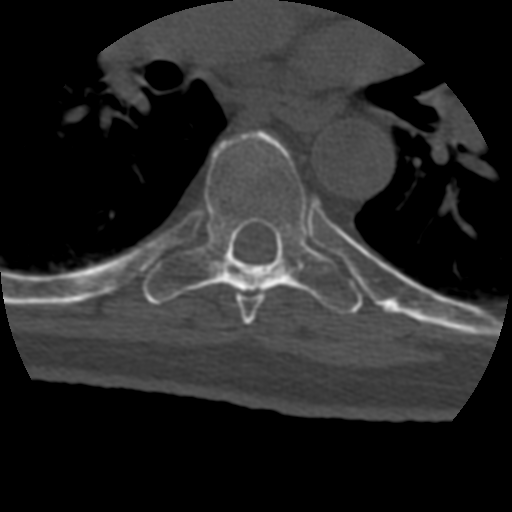
CT including the spine, one axial slice. Slice 287 of 399 in the series (ordered by position). Bone window (W 1800 / L 400 HU). 1.25 mm slice thickness. 512 × 512 image matrix. Patient age 69 years. Case-level facts recorded for this patient, not image findings: primary cancer: prostate.
Structures marked on this image (semi-automatic segmentation, software-assisted and operator-edited):
- T6 vertebra: box from (x=222, y=283) to (x=264, y=325) px
- T7 vertebra: (x=143, y=131)–(x=363, y=314)